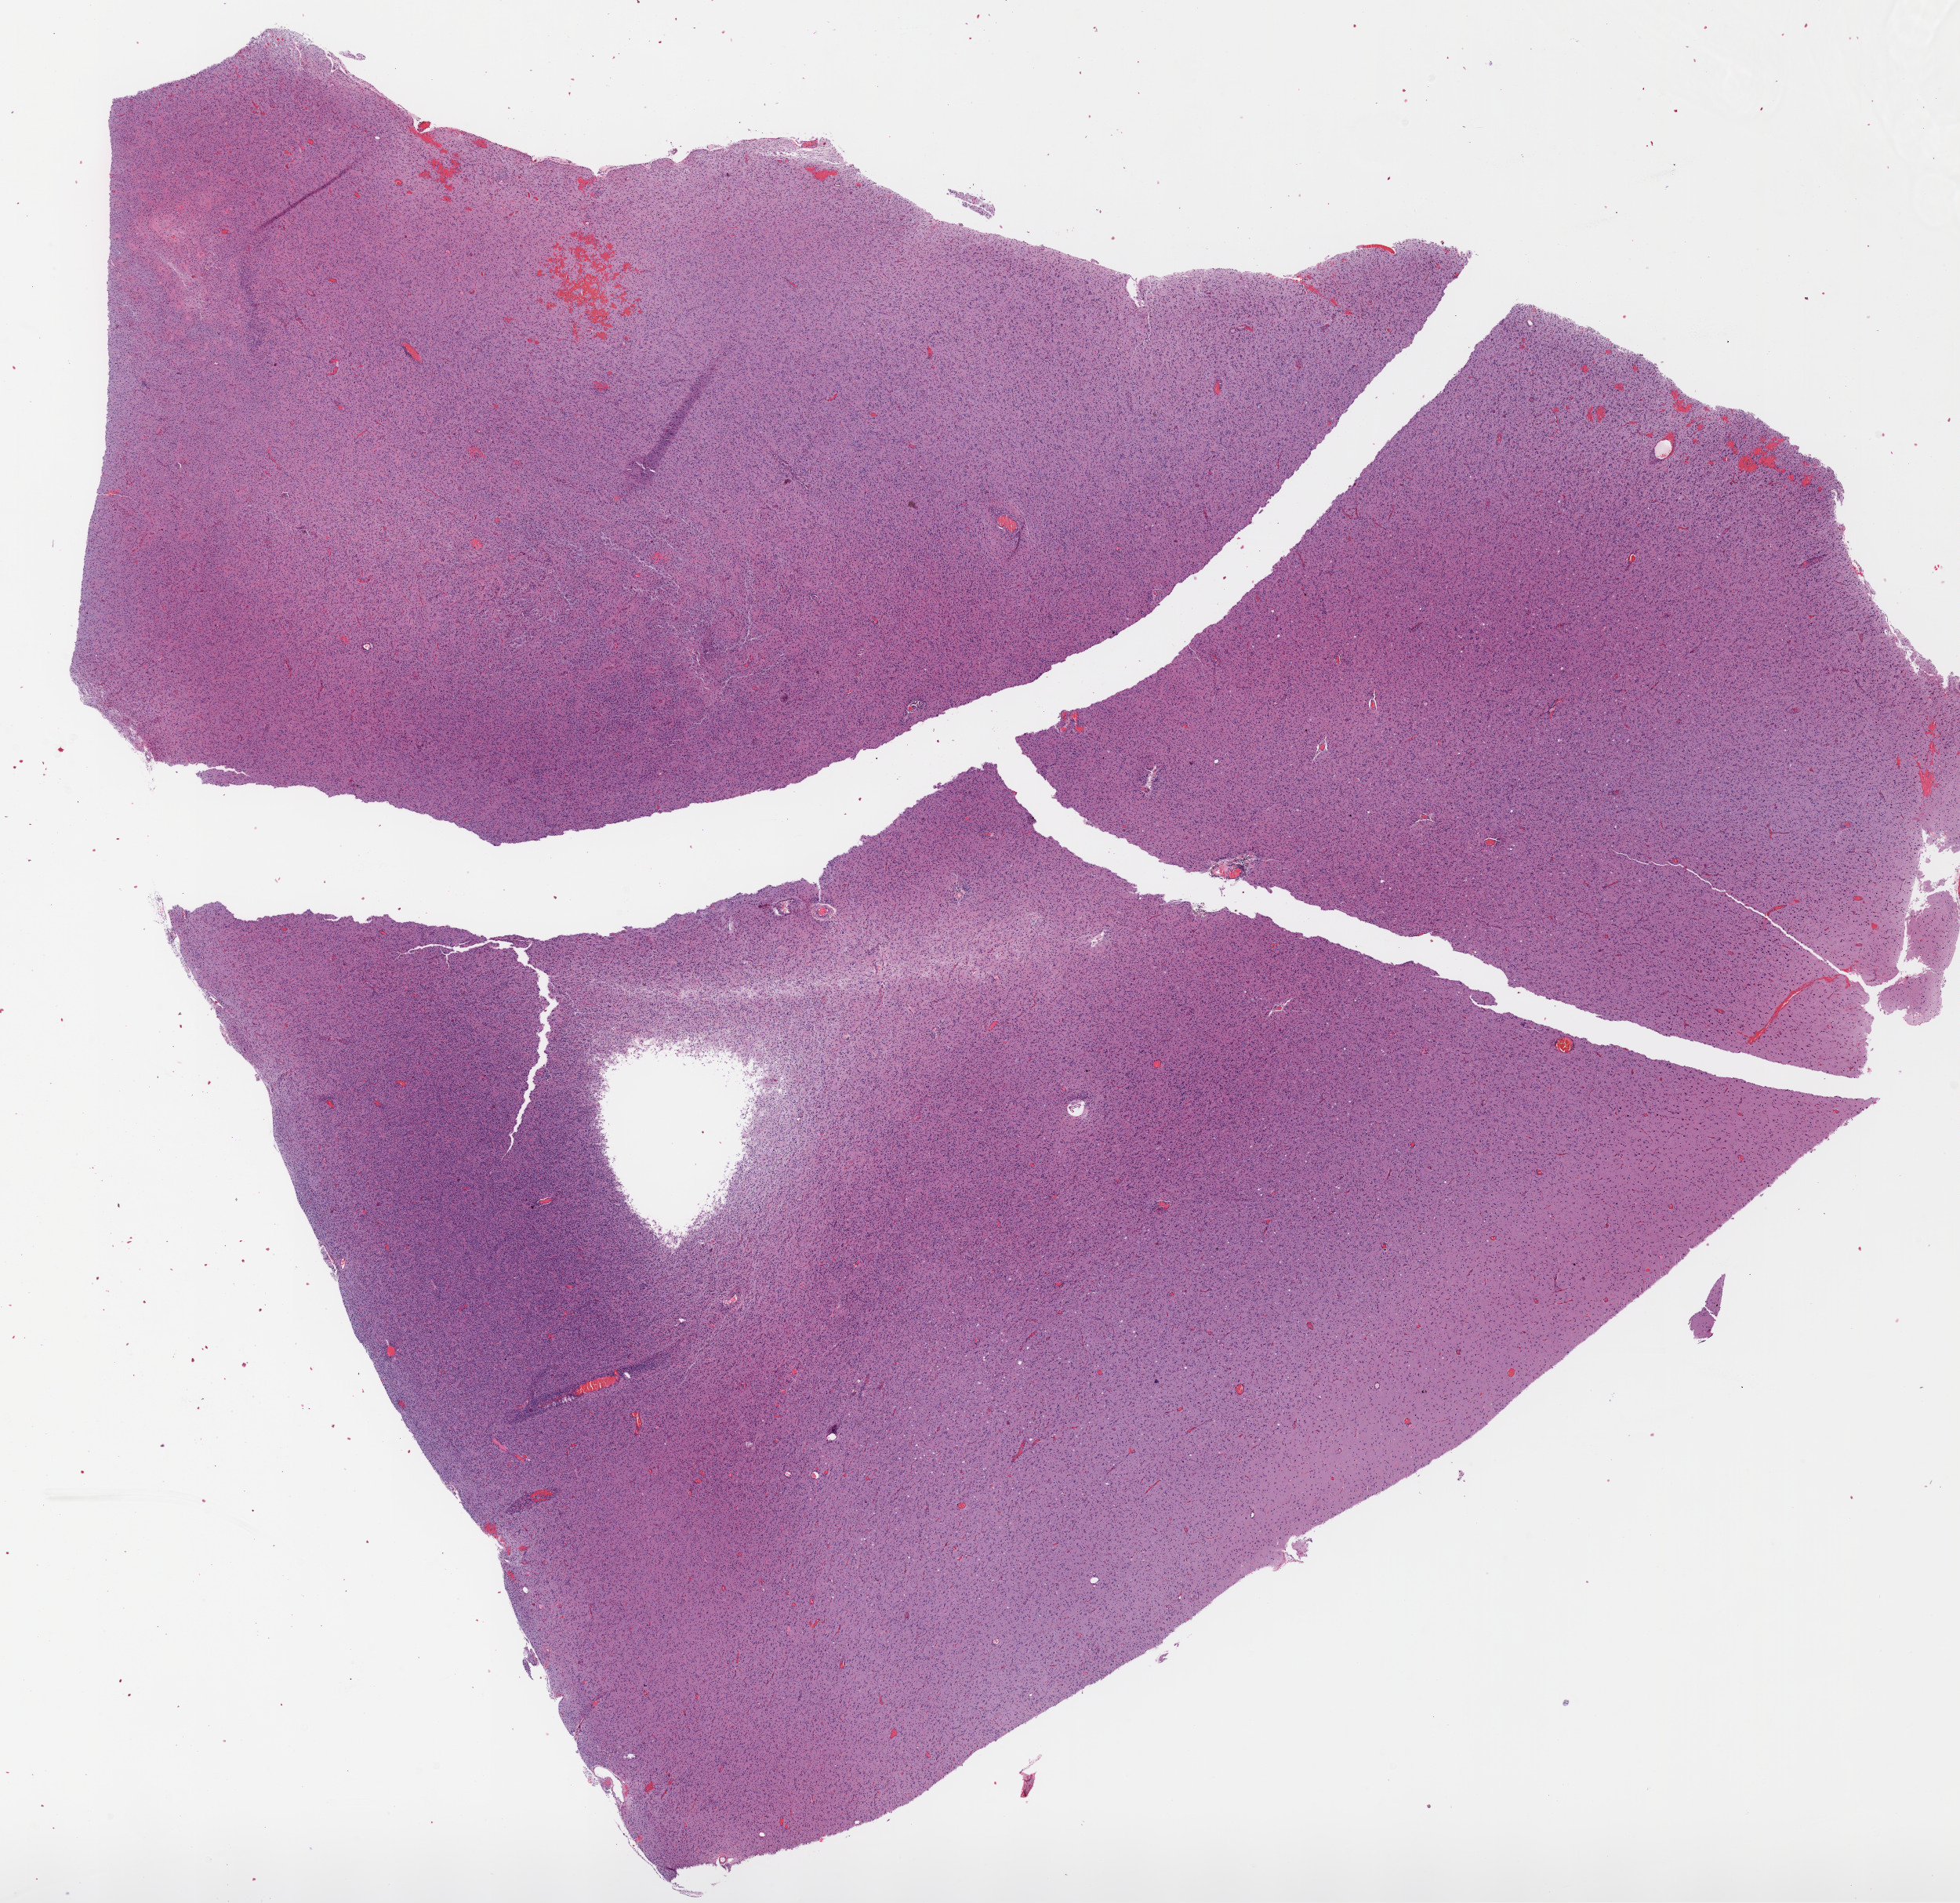
Whole-slide histology image, H&E-stained, a low-resolution overview of the entire scanned area, about 20.1 x 19.5 mm; FFPE section; sample: primary tumour, brain. Patient: male, age at initial diagnosis 57 years.
Histologic diagnosis: Glioblastoma.